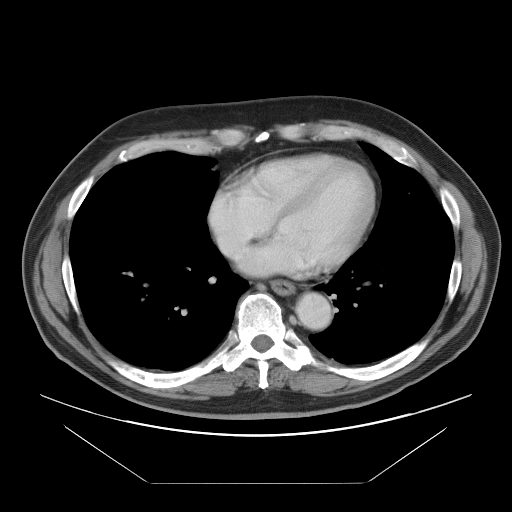
Contrast-enhanced abdominal CT, one axial slice; slice 96 of 97 in the series (ordered by position); 120 kVp; intravenous contrast given; soft-tissue window (W 400 / L 40 HU); 5 mm slice thickness; 512 × 512 image matrix, field of view 442 × 442 mm. Male patient, age 62 years. From the clinical record (not read from this slice): diagnosis: colorectal cancer liver metastases, imaged before liver resection; multiple liver metastases: no; largest metastasis: 7 cm; chemotherapy before resection: yes.
Annotated regions visible in this slice (expert manual segmentation):
- hepatic veins: bounding box [x1, y1, x2, y2] px = [211, 185, 247, 272]